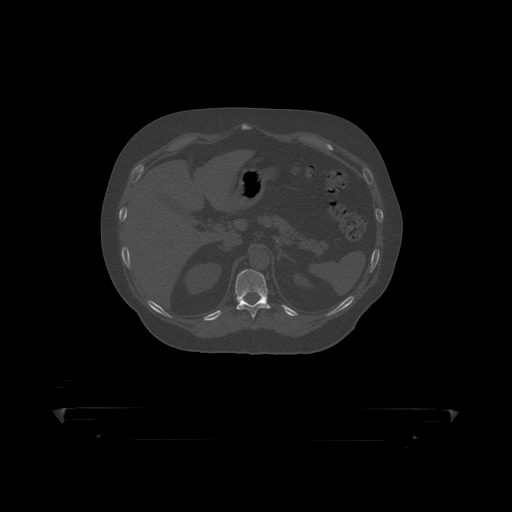
CT including the spine, one axial slice; slice 194 of 390 in the series (ordered by position); 120 kVp; bone window (W 1800 / L 400 HU); 1.25 mm slice thickness; 512 × 512 image matrix. Patient: male, 60 years. From the clinical record (not read from this slice): primary cancer: prostate.
Structures marked on this image (semi-automatically segmented with operator editing):
- T11 vertebra: box from (x=235, y=269) to (x=290, y=319) px